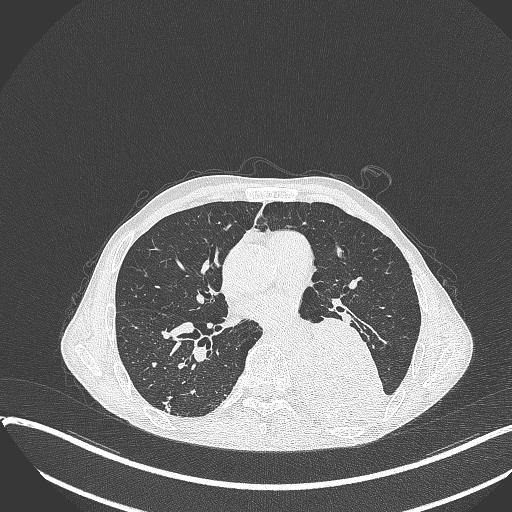
Chest CT, one axial slice; slice 184 of 401 in the series (ordered by position); reconstruction kernel B70f; 120 kVp; lung window (W 1500 / L -600 HU); 1 mm slice thickness; 512 × 512 image matrix, field of view 400 × 400 mm. Male patient, age 57 years. Case-level facts recorded for this patient, not image findings: clinical TNM (as recorded): T4 N0 M0.
Outlined on this slice (rectangle marked by the reading radiologist):
- lung tumour (recorded histology: squamous cell carcinoma): bounding box <291,311,390,430> (left, top, right, bottom; pixels)